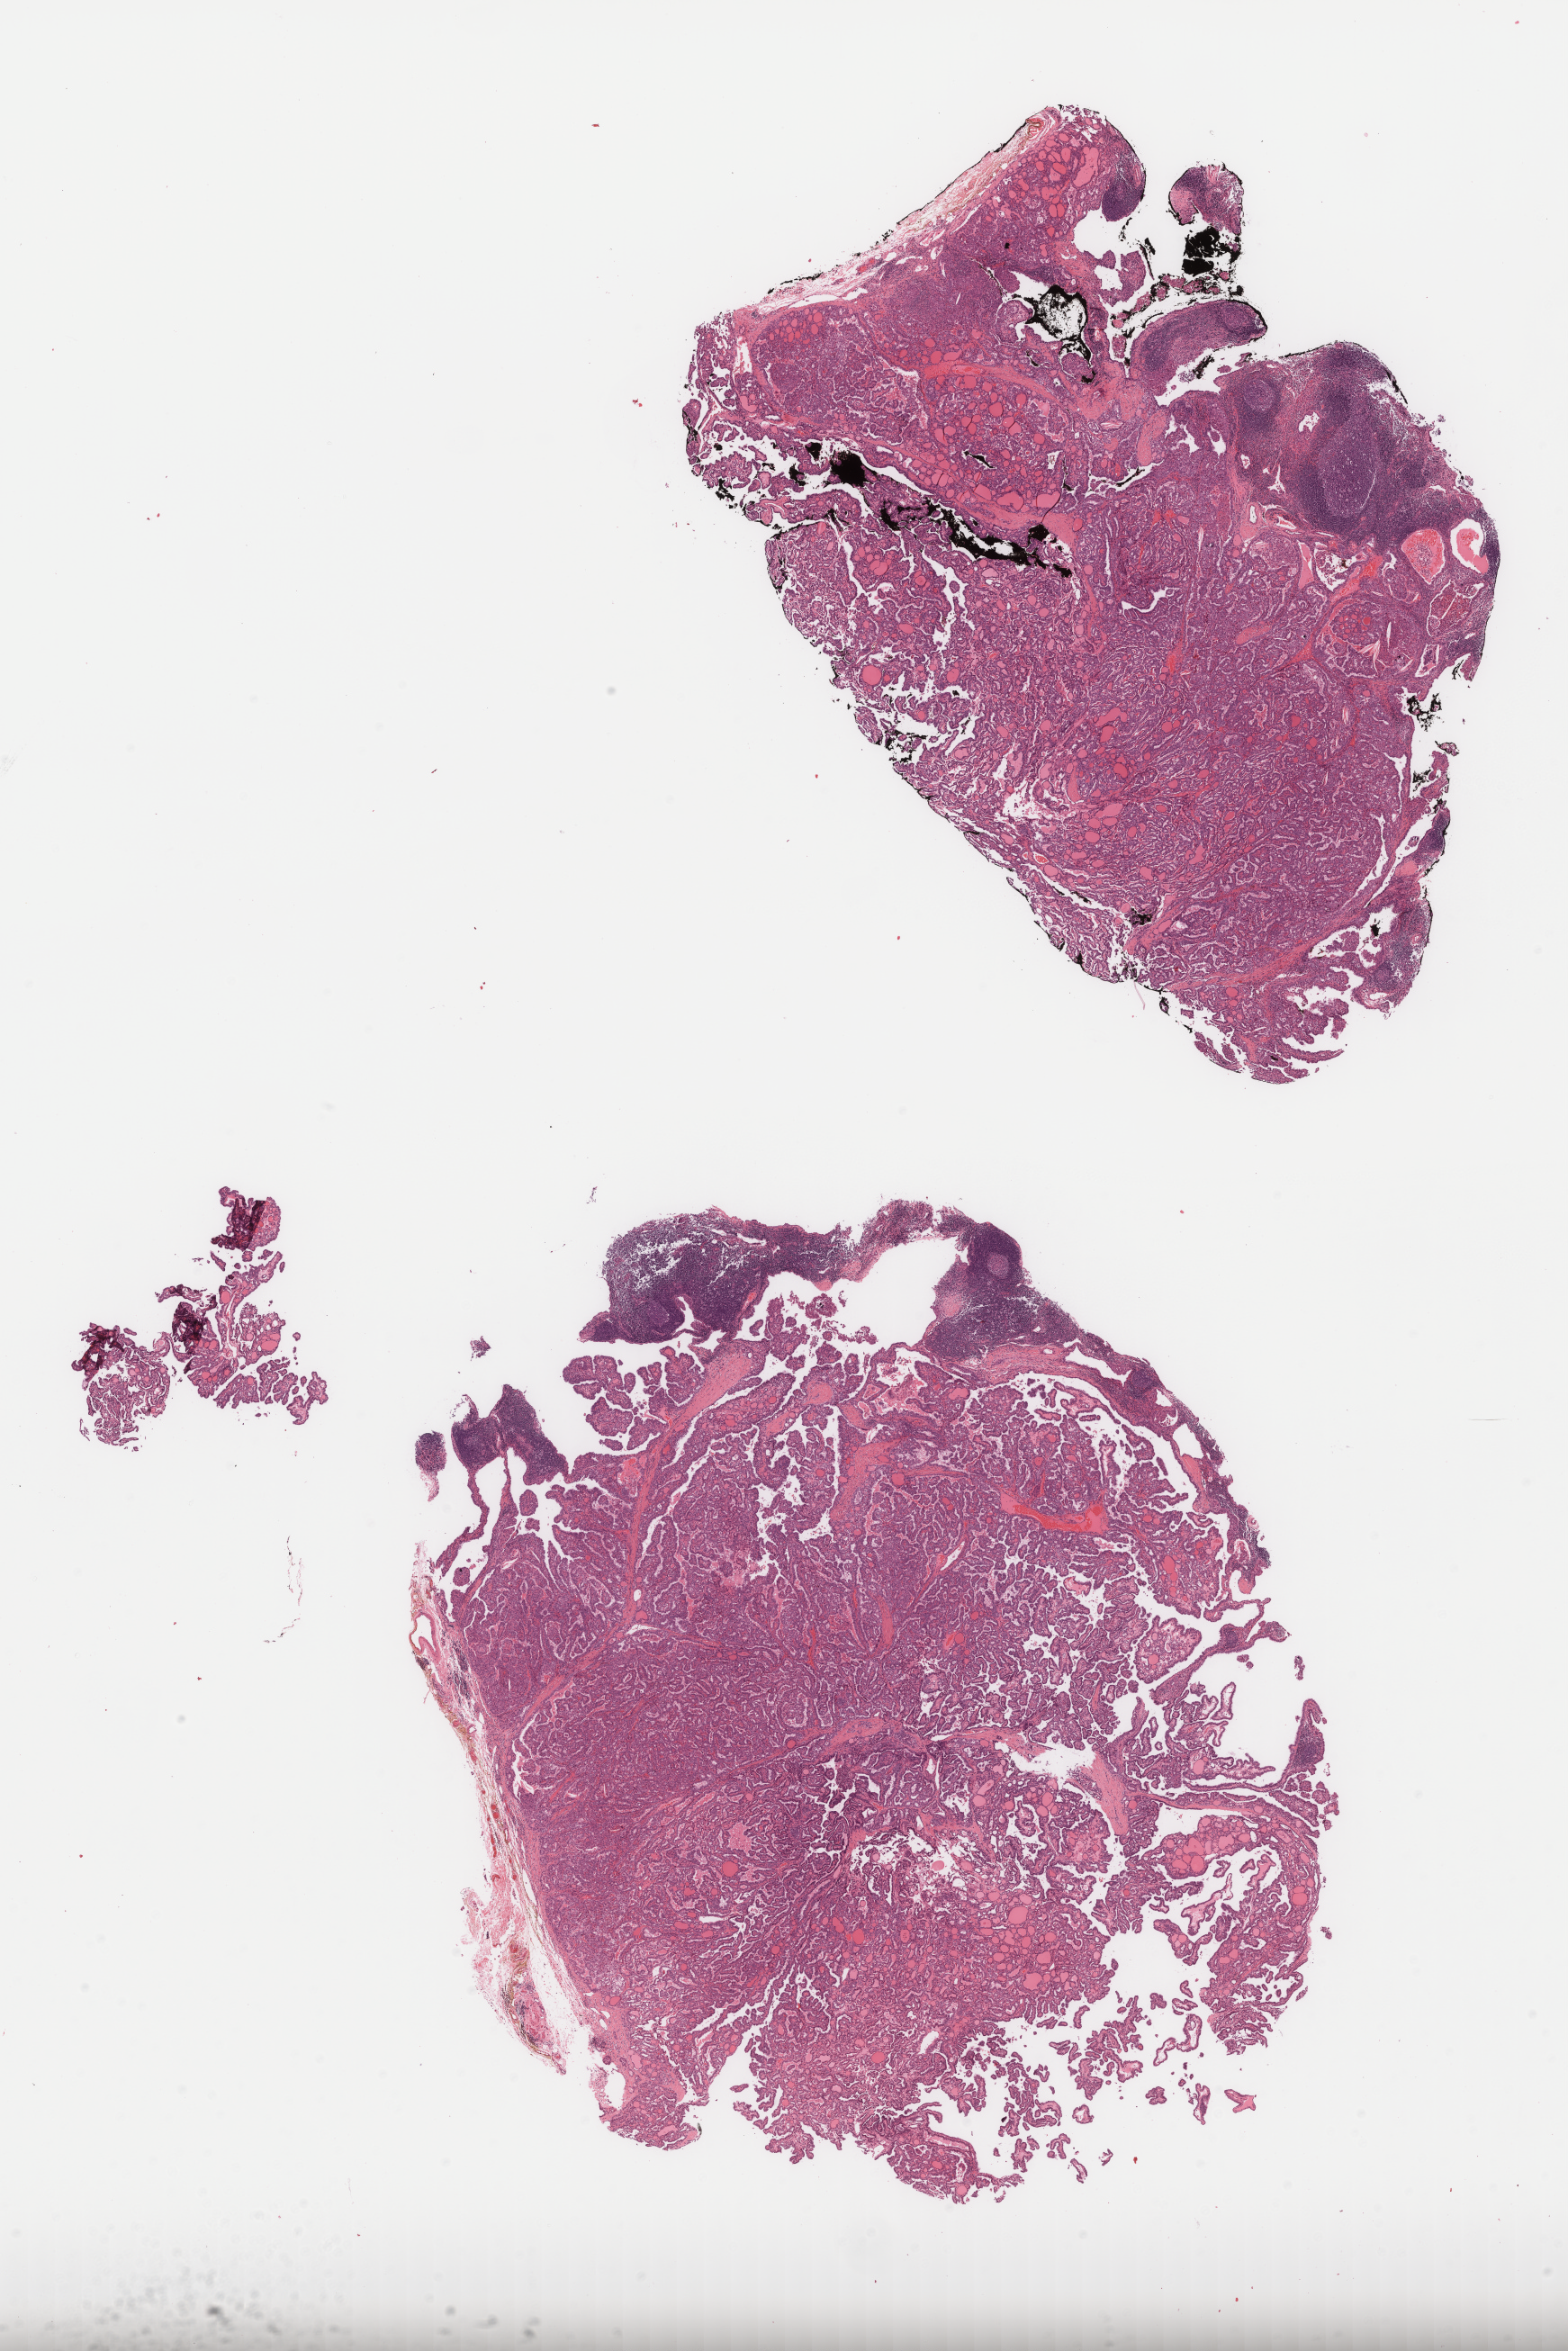
Digitized H&E tissue section (whole slide), shown as a low-resolution overview of the whole scanned area (about 14.0 x 21.0 mm, acquisition: 40x scan); formalin-fixed paraffin-embedded (FFPE) diagnostic section; thyroid, primary tumour sample. Female patient; age at initial diagnosis 19 years.
- AJCC pathologic stage: I (7th edition)
- histologic diagnosis: Papillary adenocarcinoma, NOS (thyroid gland)
- TNM: T3 N1b MX
- lymph nodes positive (case pathology): 41 of 66 examined